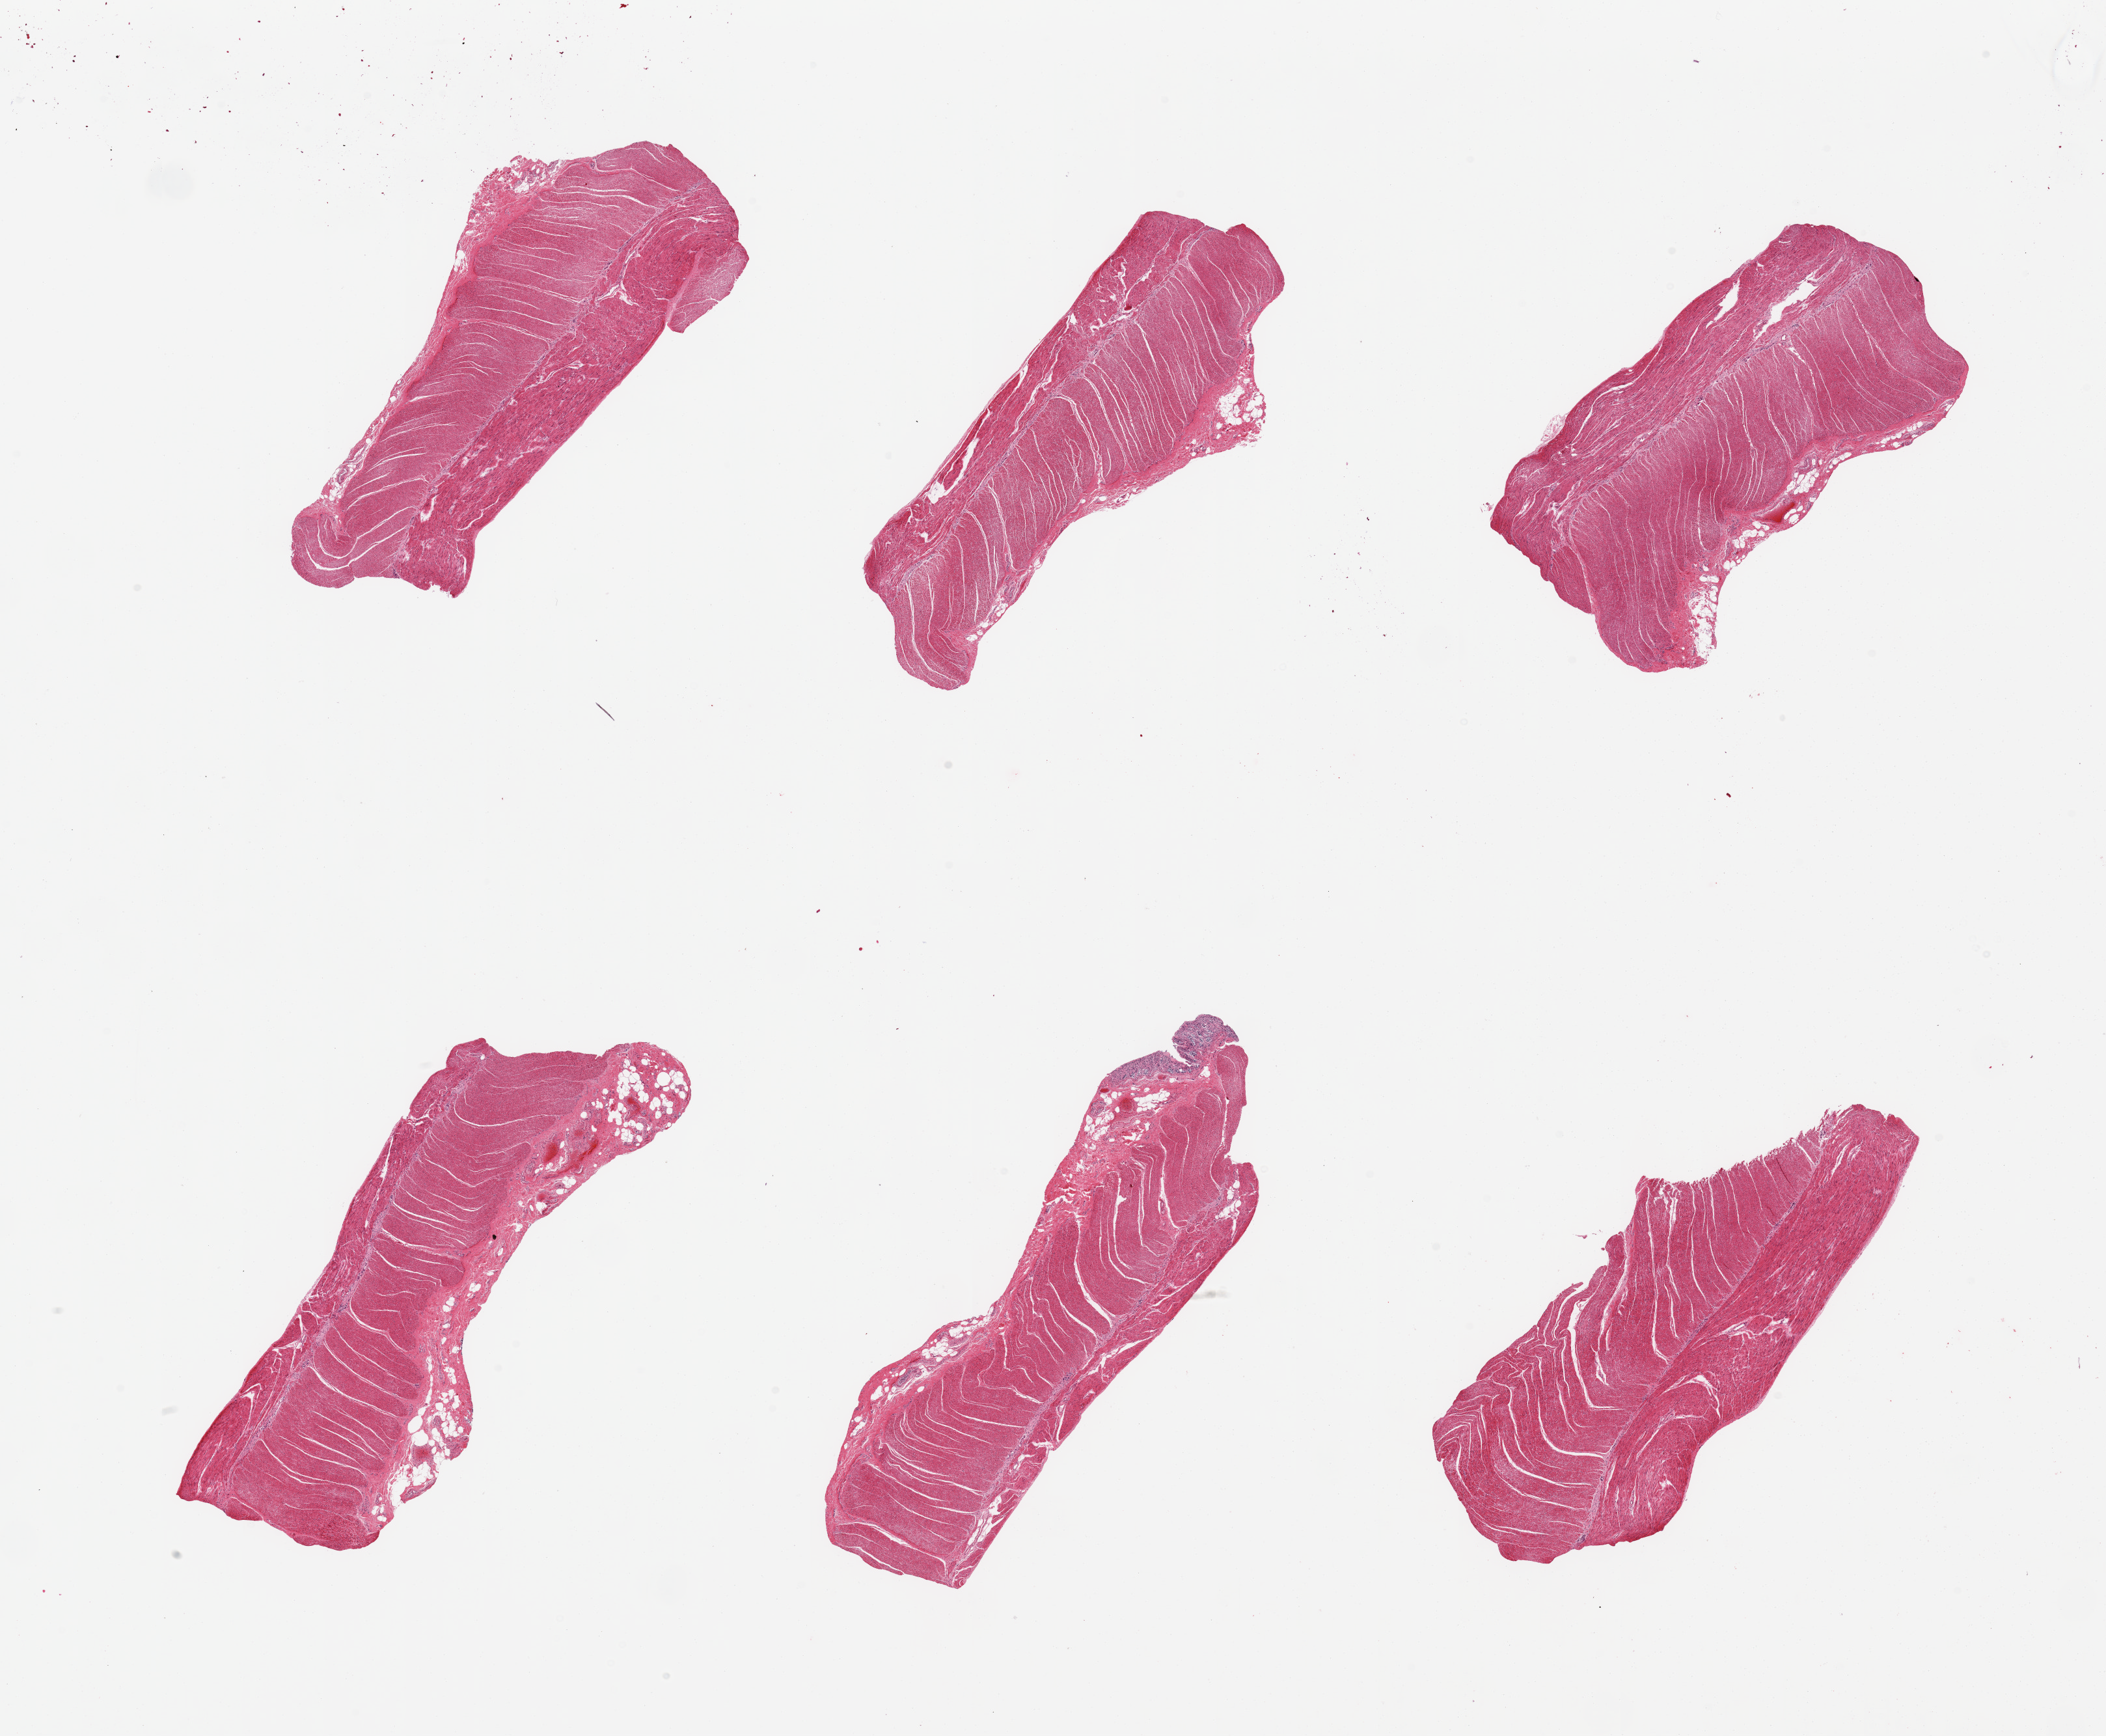
H&E whole-slide image, brightfield — shown as a low-resolution overview of the whole scanned area (about 25.6 x 21.1 mm). PAXgene-fixed, paraffin-embedded tissue. Target tissue: sigmoid colon. Donor tissue sample. Donor sex: male.
Review note (as recorded): 6 pieces, confirmed target muscularis.